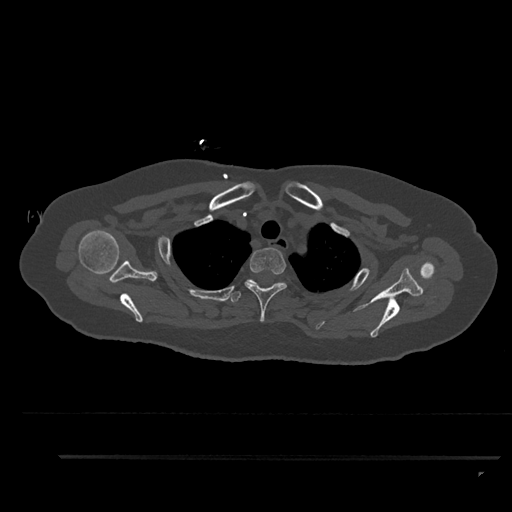
CT including the spine, one axial slice. Position 714 of 797 along the scan axis. Reconstruction kernel Br40s/3. Bone window (W 1800 / L 400 HU). 512 × 512 image matrix, field of view 408 × 408 mm. Patient: female, 44 years. Case-level facts recorded for this patient, not image findings: primary cancer: renal; vertebrae with lytic lesions (as recorded): L1.
Outlined on this slice (semi-automatically segmented with operator editing):
- T1 vertebra: bounding box [x1, y1, x2, y2] px = [271, 283, 278, 287]
- T2 vertebra: [245, 248, 287, 322]
- T3 vertebra: [227, 279, 256, 302]